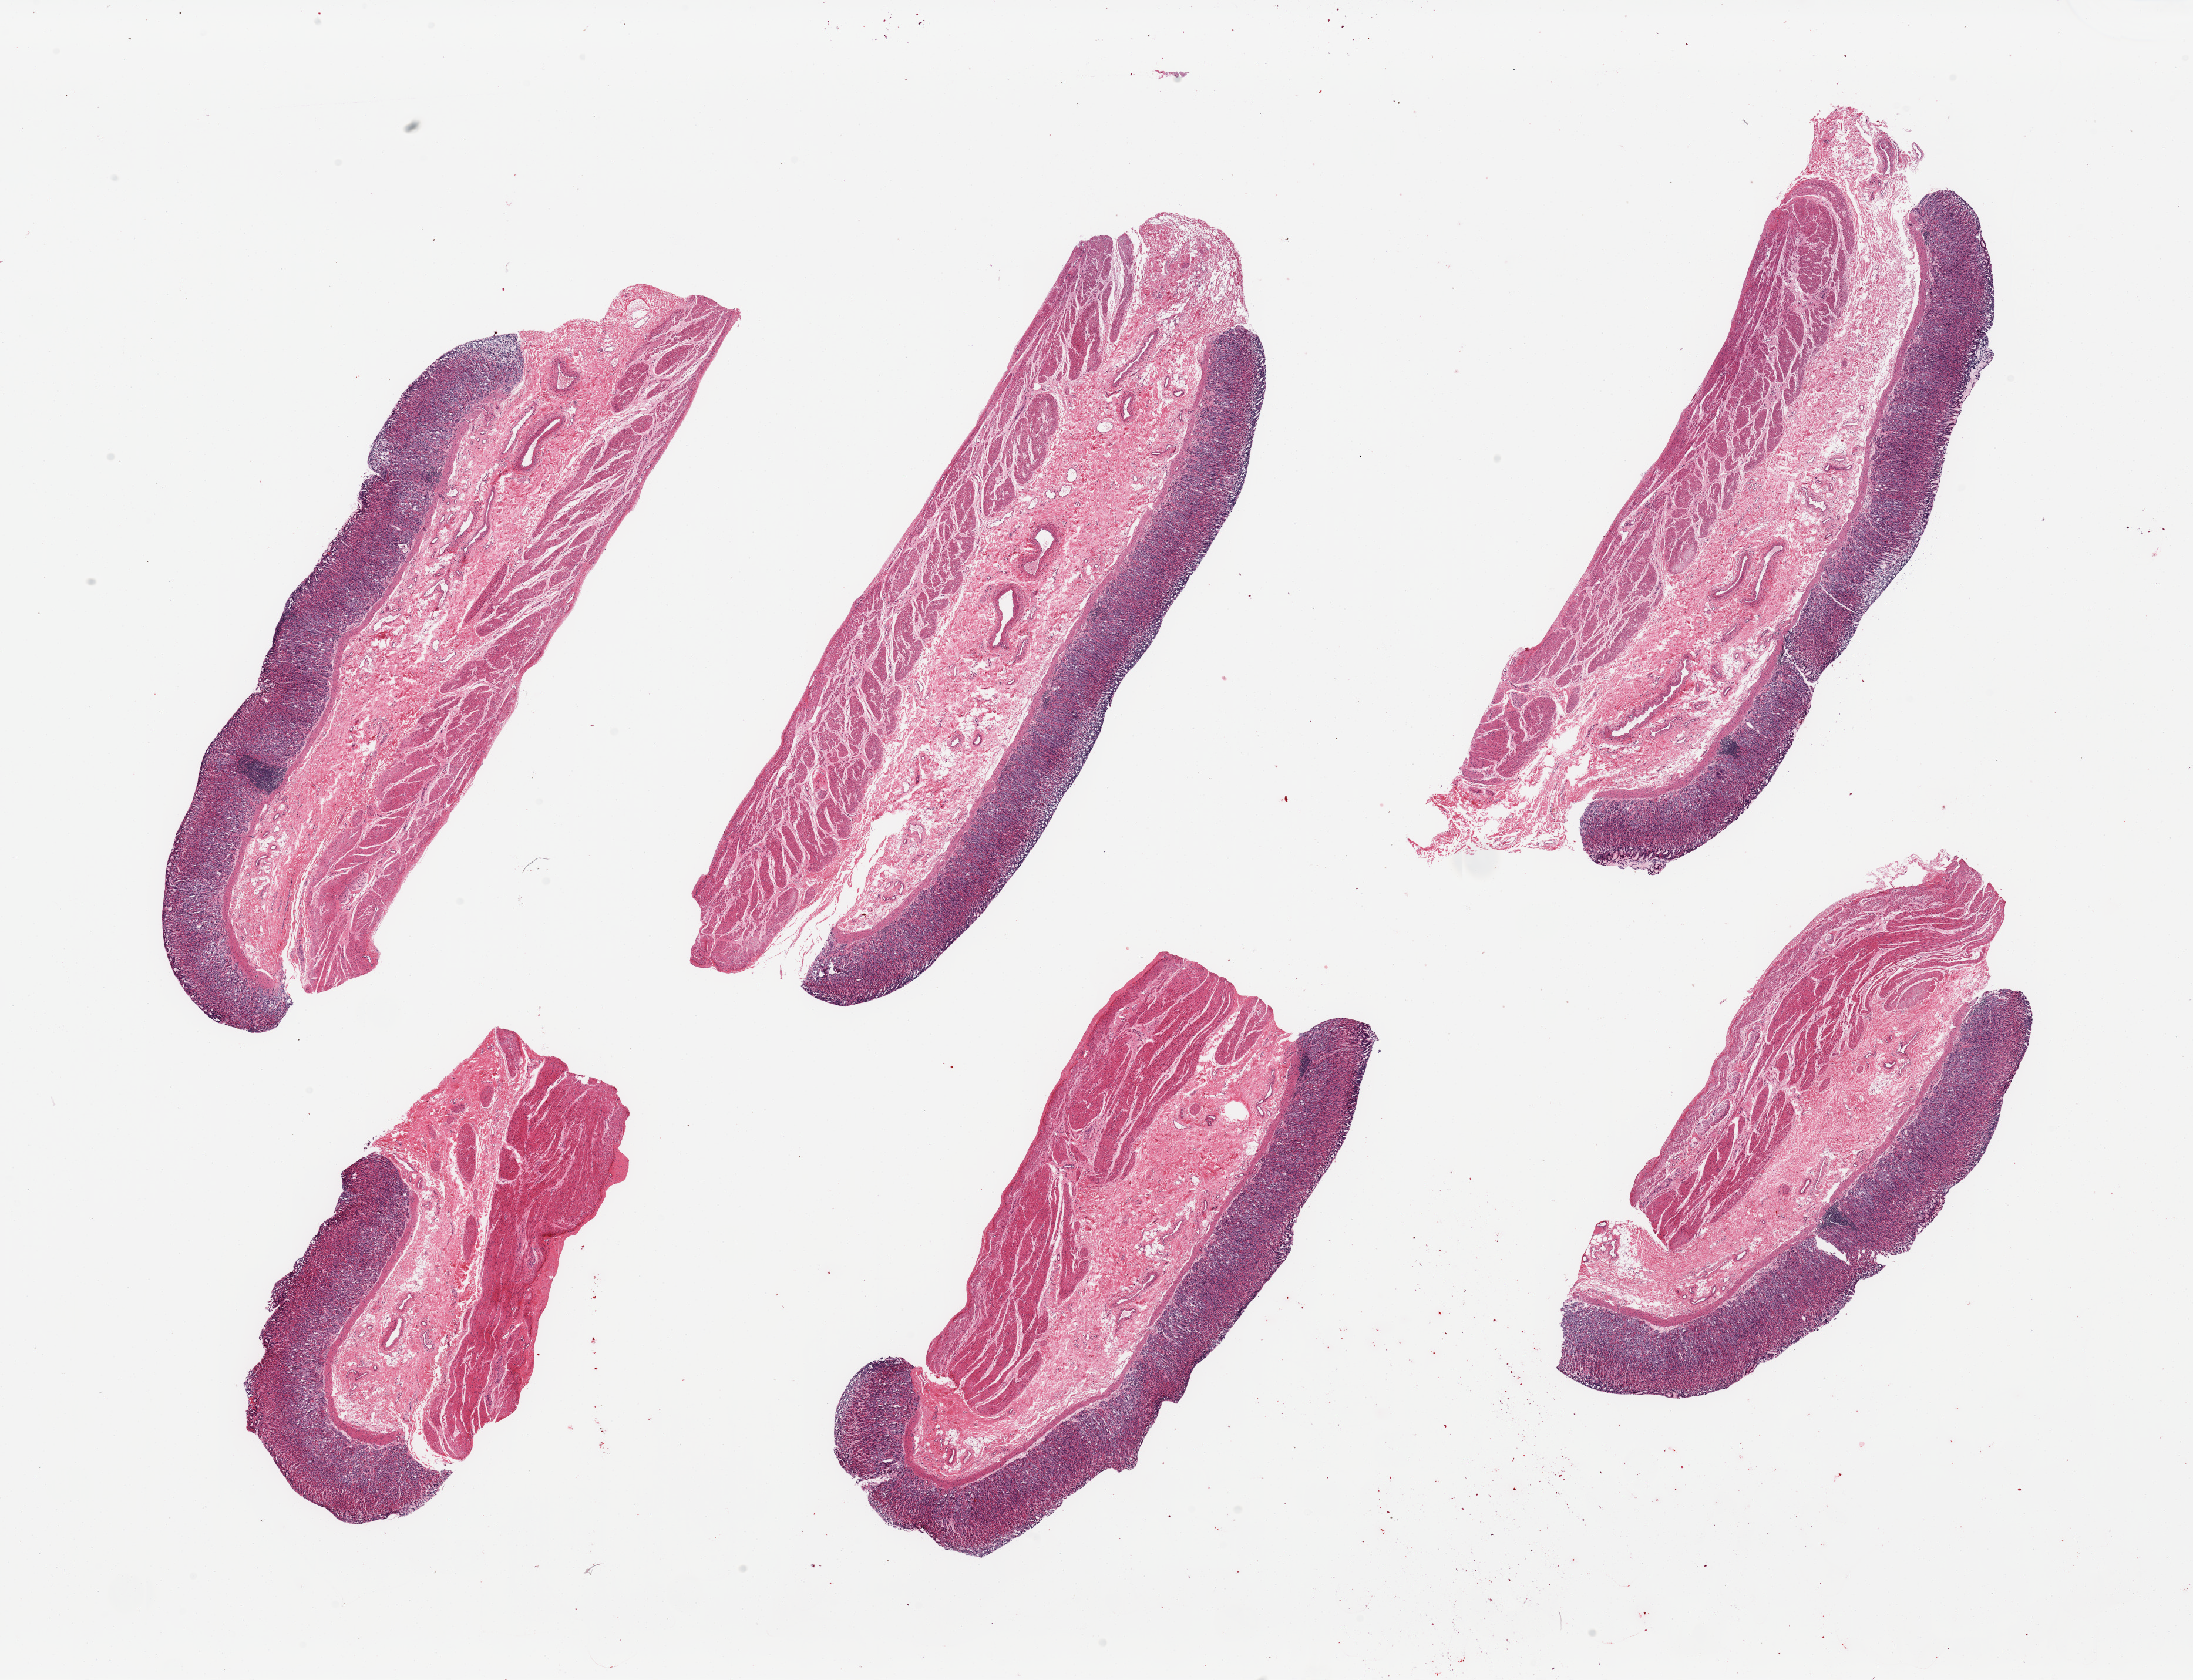
Haematoxylin and eosin whole-slide image — shown as a low-resolution overview of the whole scanned area (about 29.5 x 22.6 mm, slide scanned at 20x); PAXgene-fixed, paraffin-embedded tissue; section of stomach (target tissue); tissue donor sample. Male donor.
* review note (as recorded): 6 pieces; full thickness sections, mild chronic gastritis